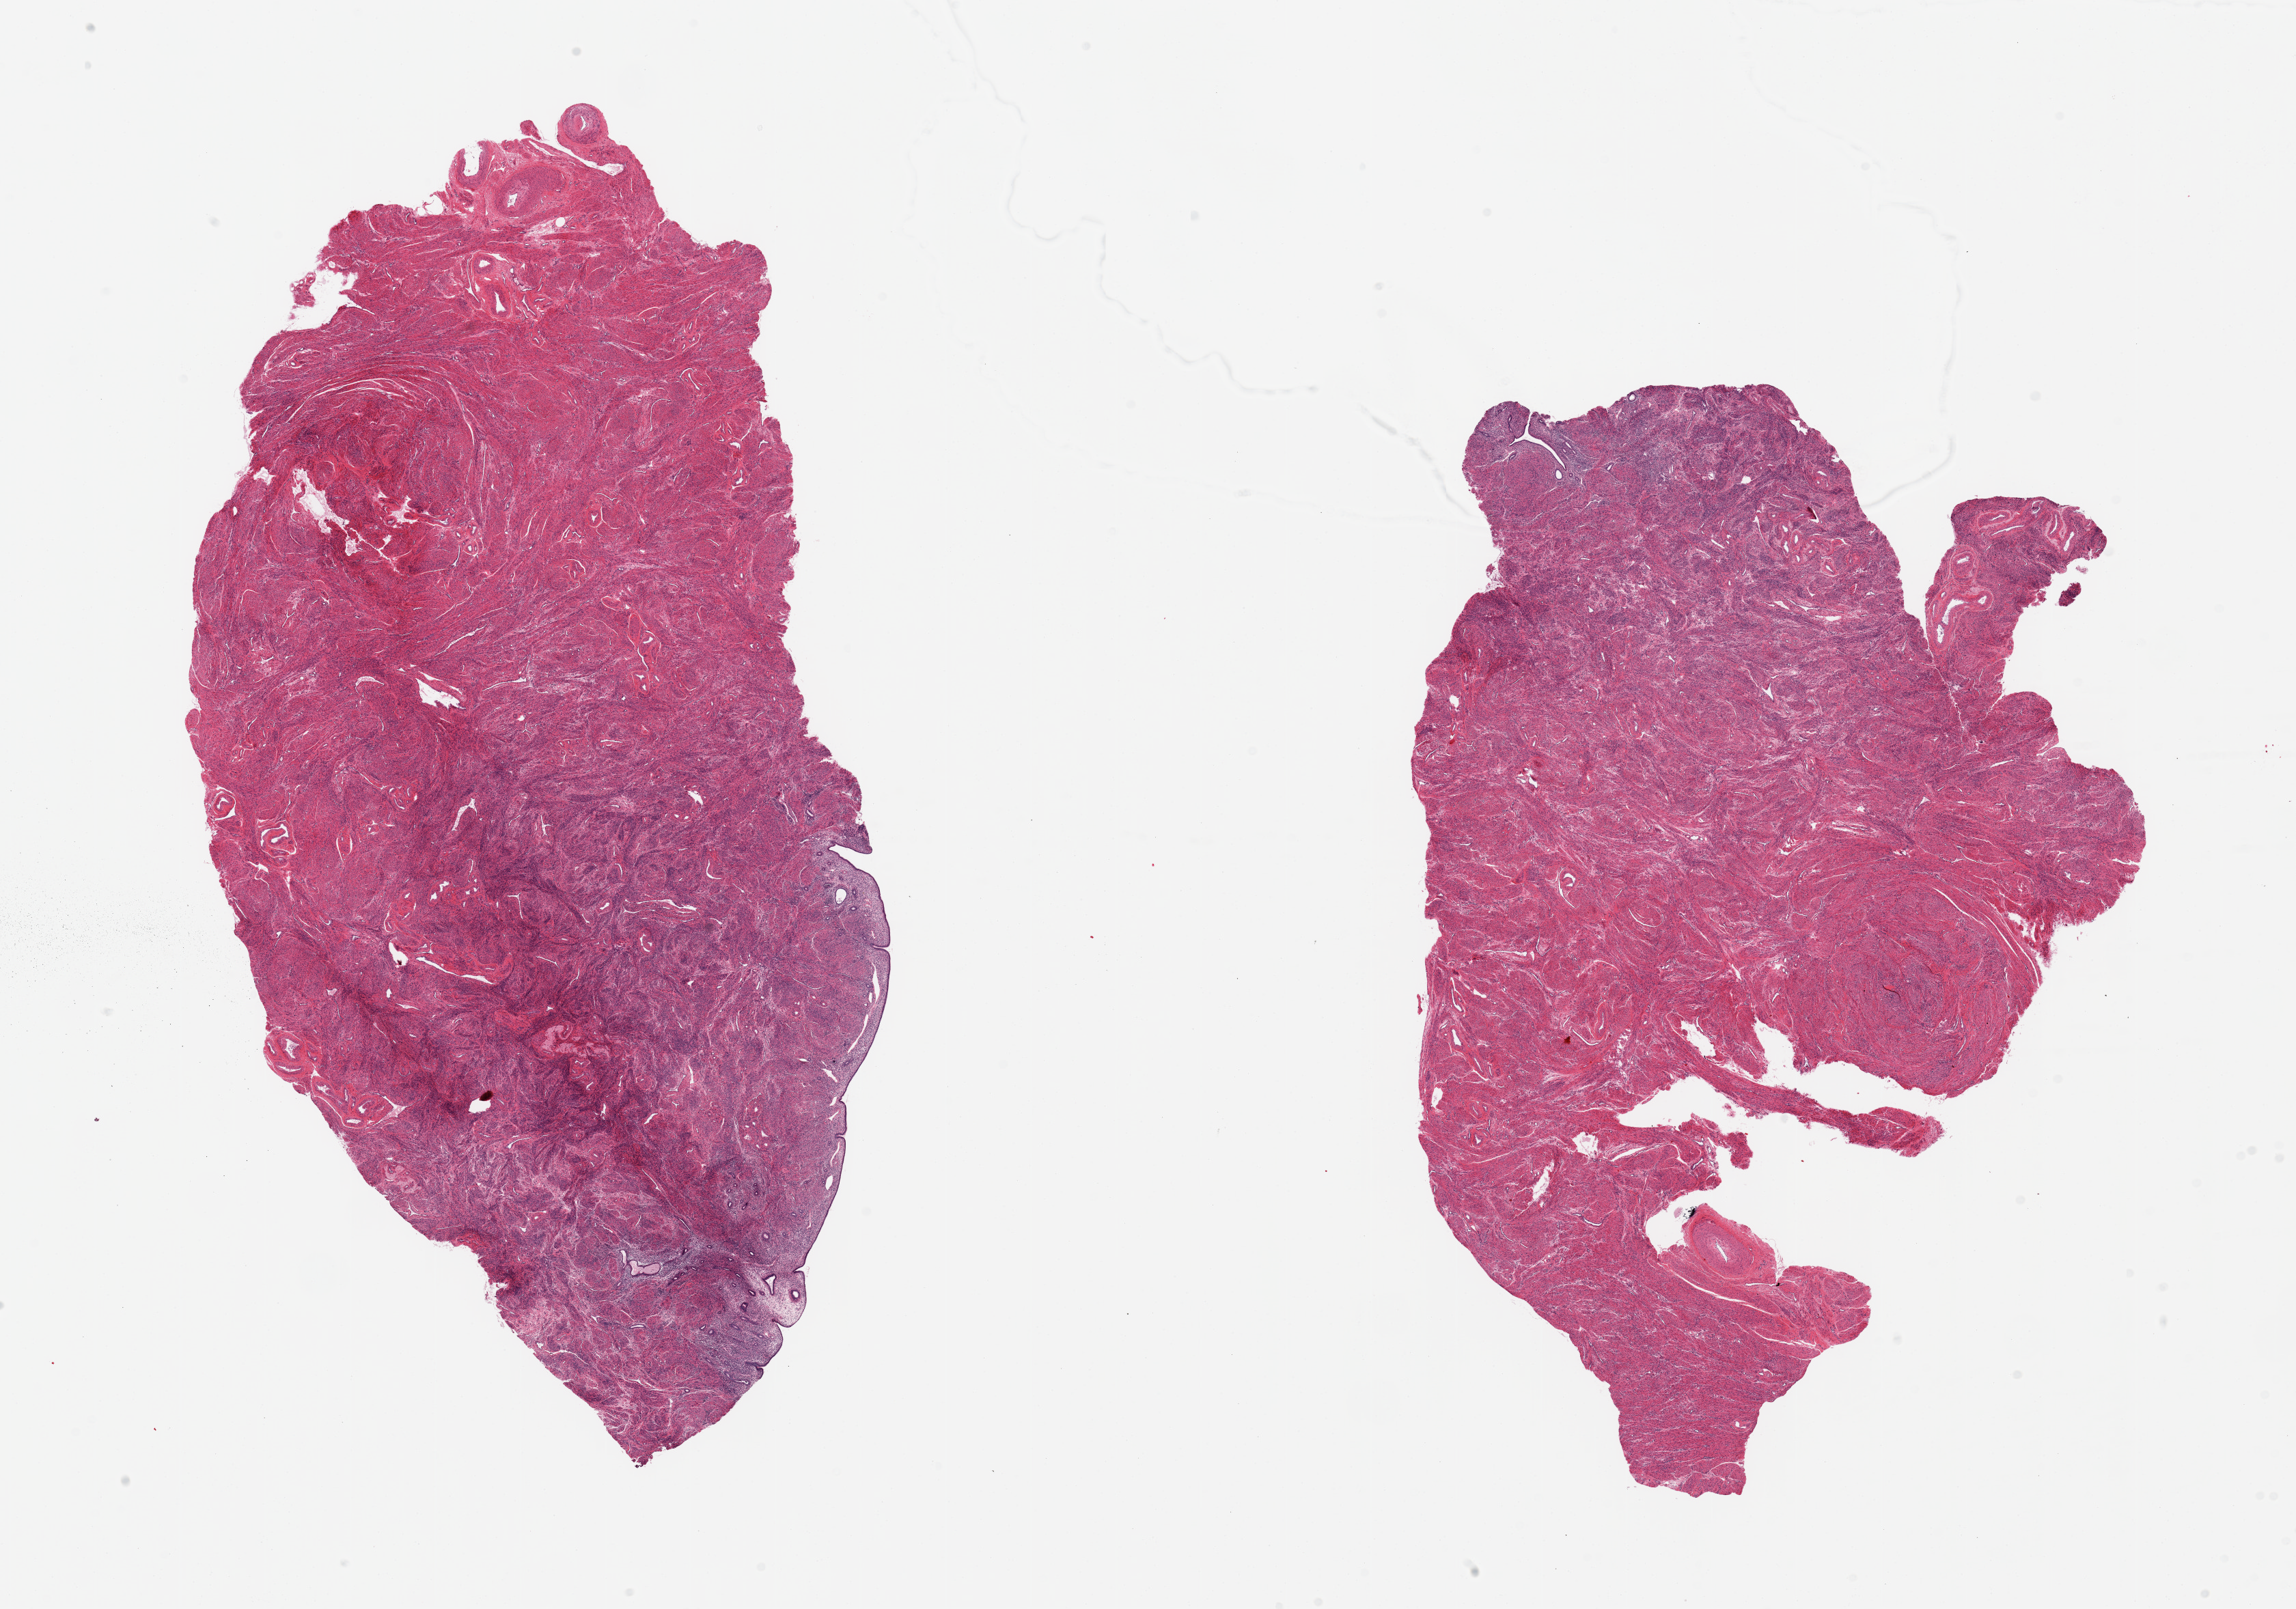
Digitized H&E-stained section — low-resolution overview of the scanned area, about 26.6 x 18.6 mm, PAXgene-fixed paraffin-embedded (PFPE) section, section of uterus (target tissue), donor tissue sample. Donor sex: female.
• pathologist's review note for this sample: 2 pieces, large myometrium, ~1.5mm thick foci of weakly proliferative endometrium